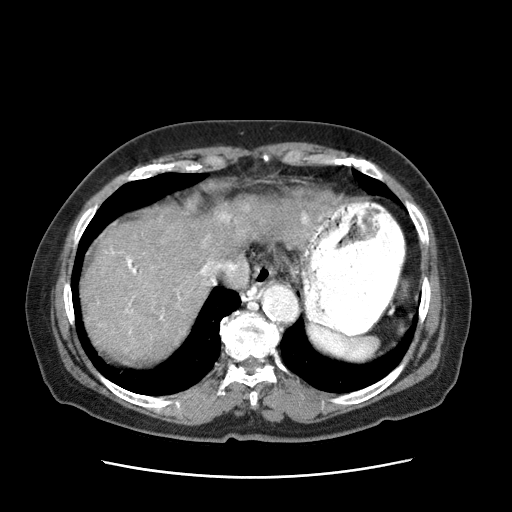
Contrast-enhanced abdominal CT (liver protocol), one axial slice. Position 57 of 63 along the scan axis. Soft-tissue window (W 400 / L 40 HU). 512 × 512 image matrix, field of view 360 × 360 mm. Patient: female, 79 years. Case-level facts recorded for this patient, not image findings: diagnosis: hepatocellular carcinoma (patient treated with transarterial chemoembolisation; whether this scan precedes or follows treatment is not stated here); TNM stage (as recorded): Stage-II; Child-Pugh class: B; tumour differentiation: well differentiated; tumour nodularity: multinodular.
Outlined on this slice (semi-automatically segmented with operator editing):
- abdominal aorta: bounding box (x1, y1, x2, y2) in pixels: (261, 285, 297, 323)
- liver parenchyma outside the tumour (the mass and vessels are separate outlines, so this box may not span the whole liver): (82, 193, 245, 369)
- mass: (211, 195, 327, 249)
- liver vessels: (97, 256, 249, 321)